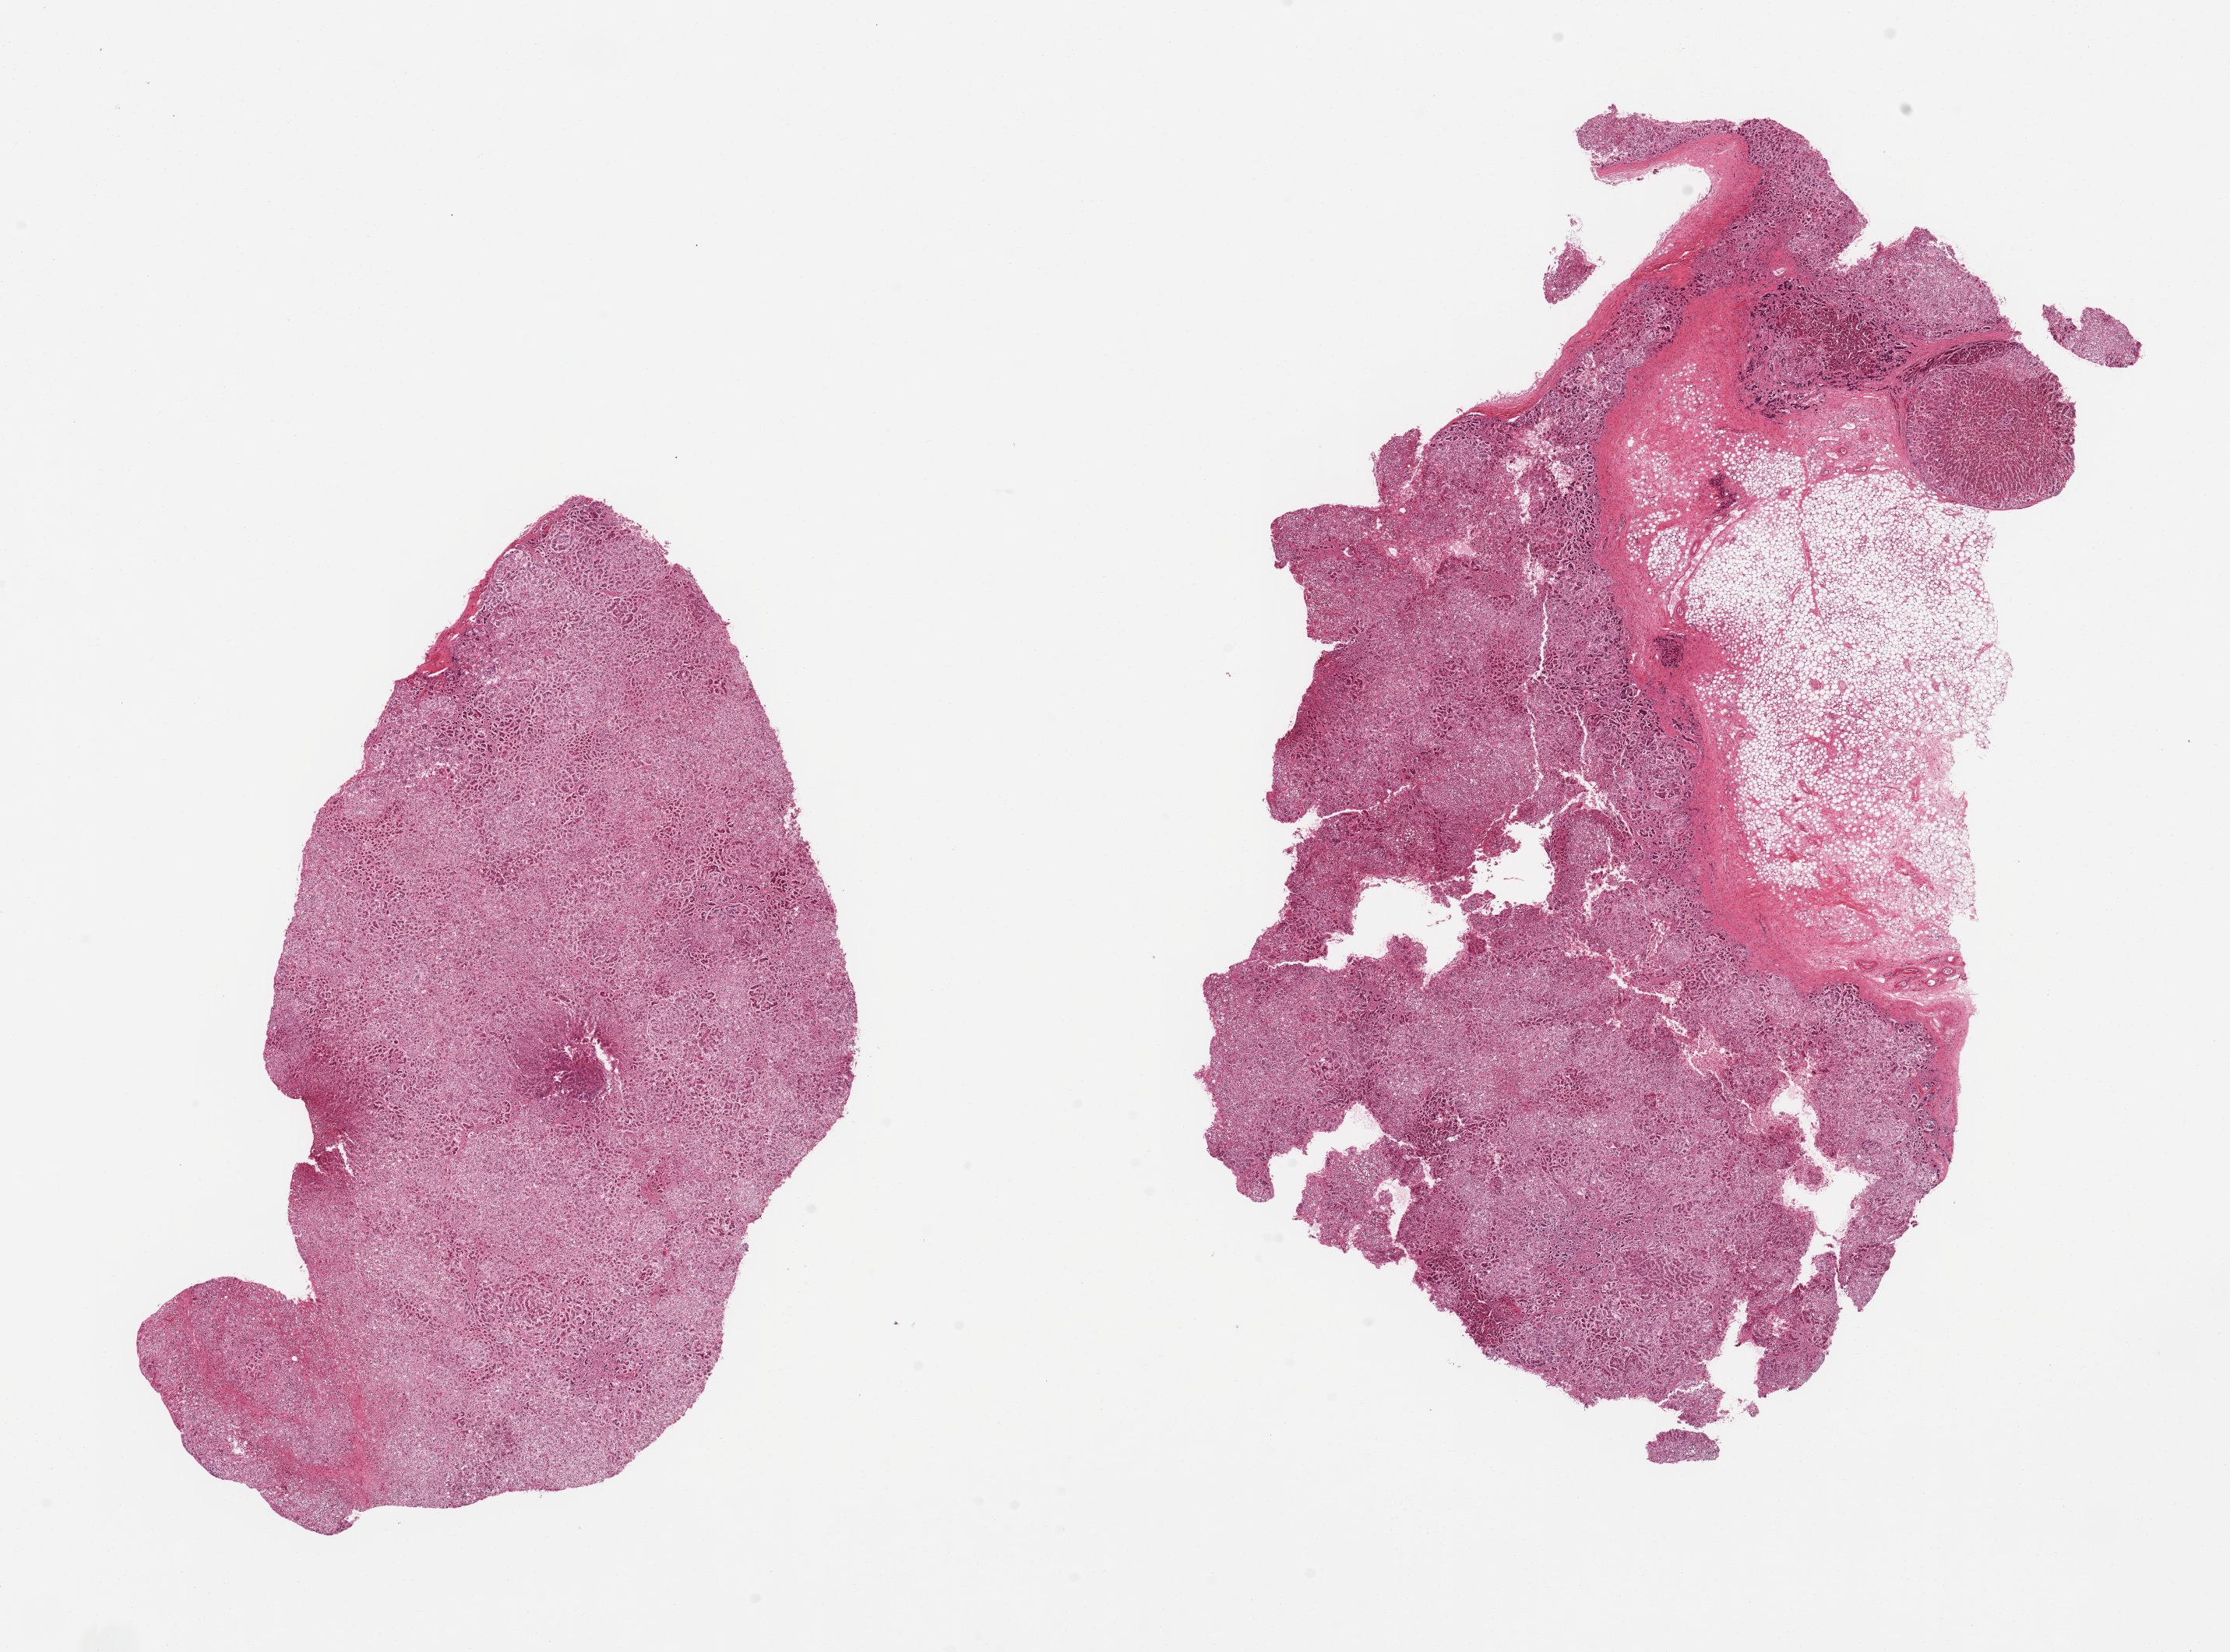
Whole-slide image, hematoxylin and eosin (H&E) stain — whole scanned area (about 22.6 x 16.8 mm) shown as a low-resolution overview; PAXgene-fixed, paraffin-embedded tissue; section of adrenal gland (target tissue); donor tissue sample. Donor sex: male.
- pathologist's review note for this sample: 2 pieces, cortex, advanced autolysis